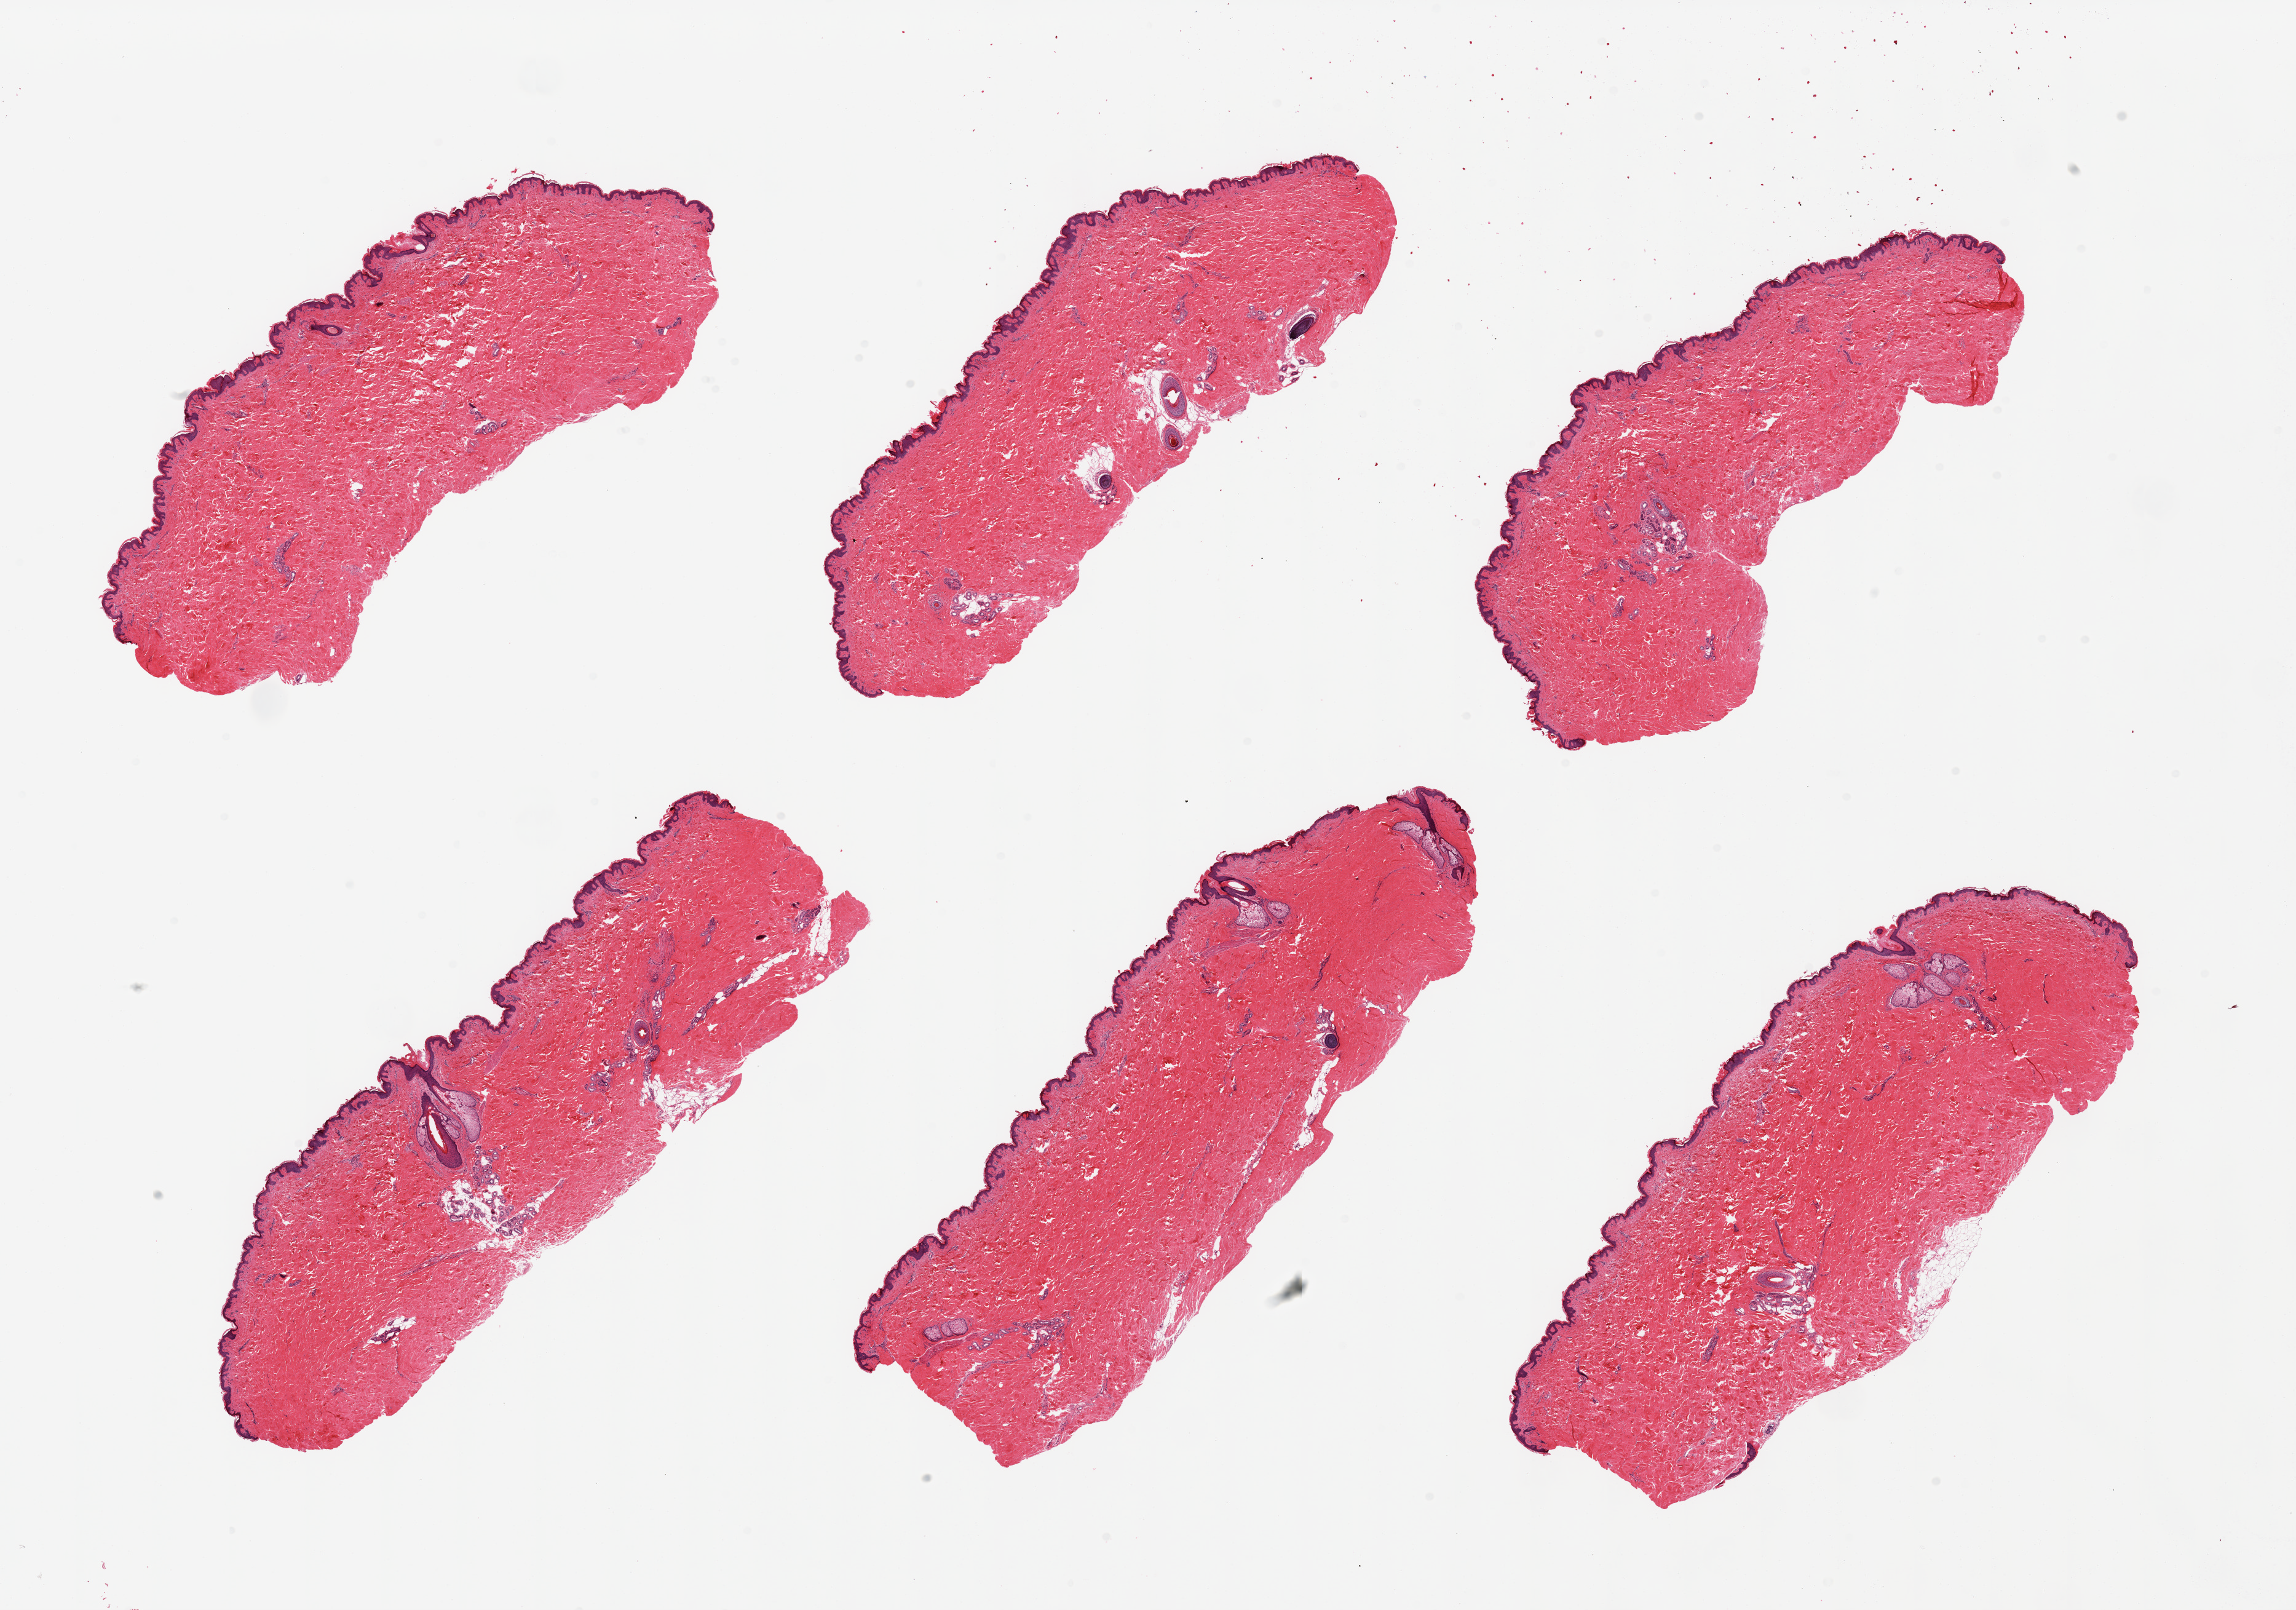
Whole-slide image, hematoxylin and eosin (H&E) stain, a low-resolution overview of the entire scanned area, about 29.5 x 20.7 mm, PAXgene-fixed, paraffin-embedded tissue, sampled site (target tissue): skin of suprapubic region, tissue donor sample.
* review note (as recorded): 6 pieces; well dissected; <5% dermal fat